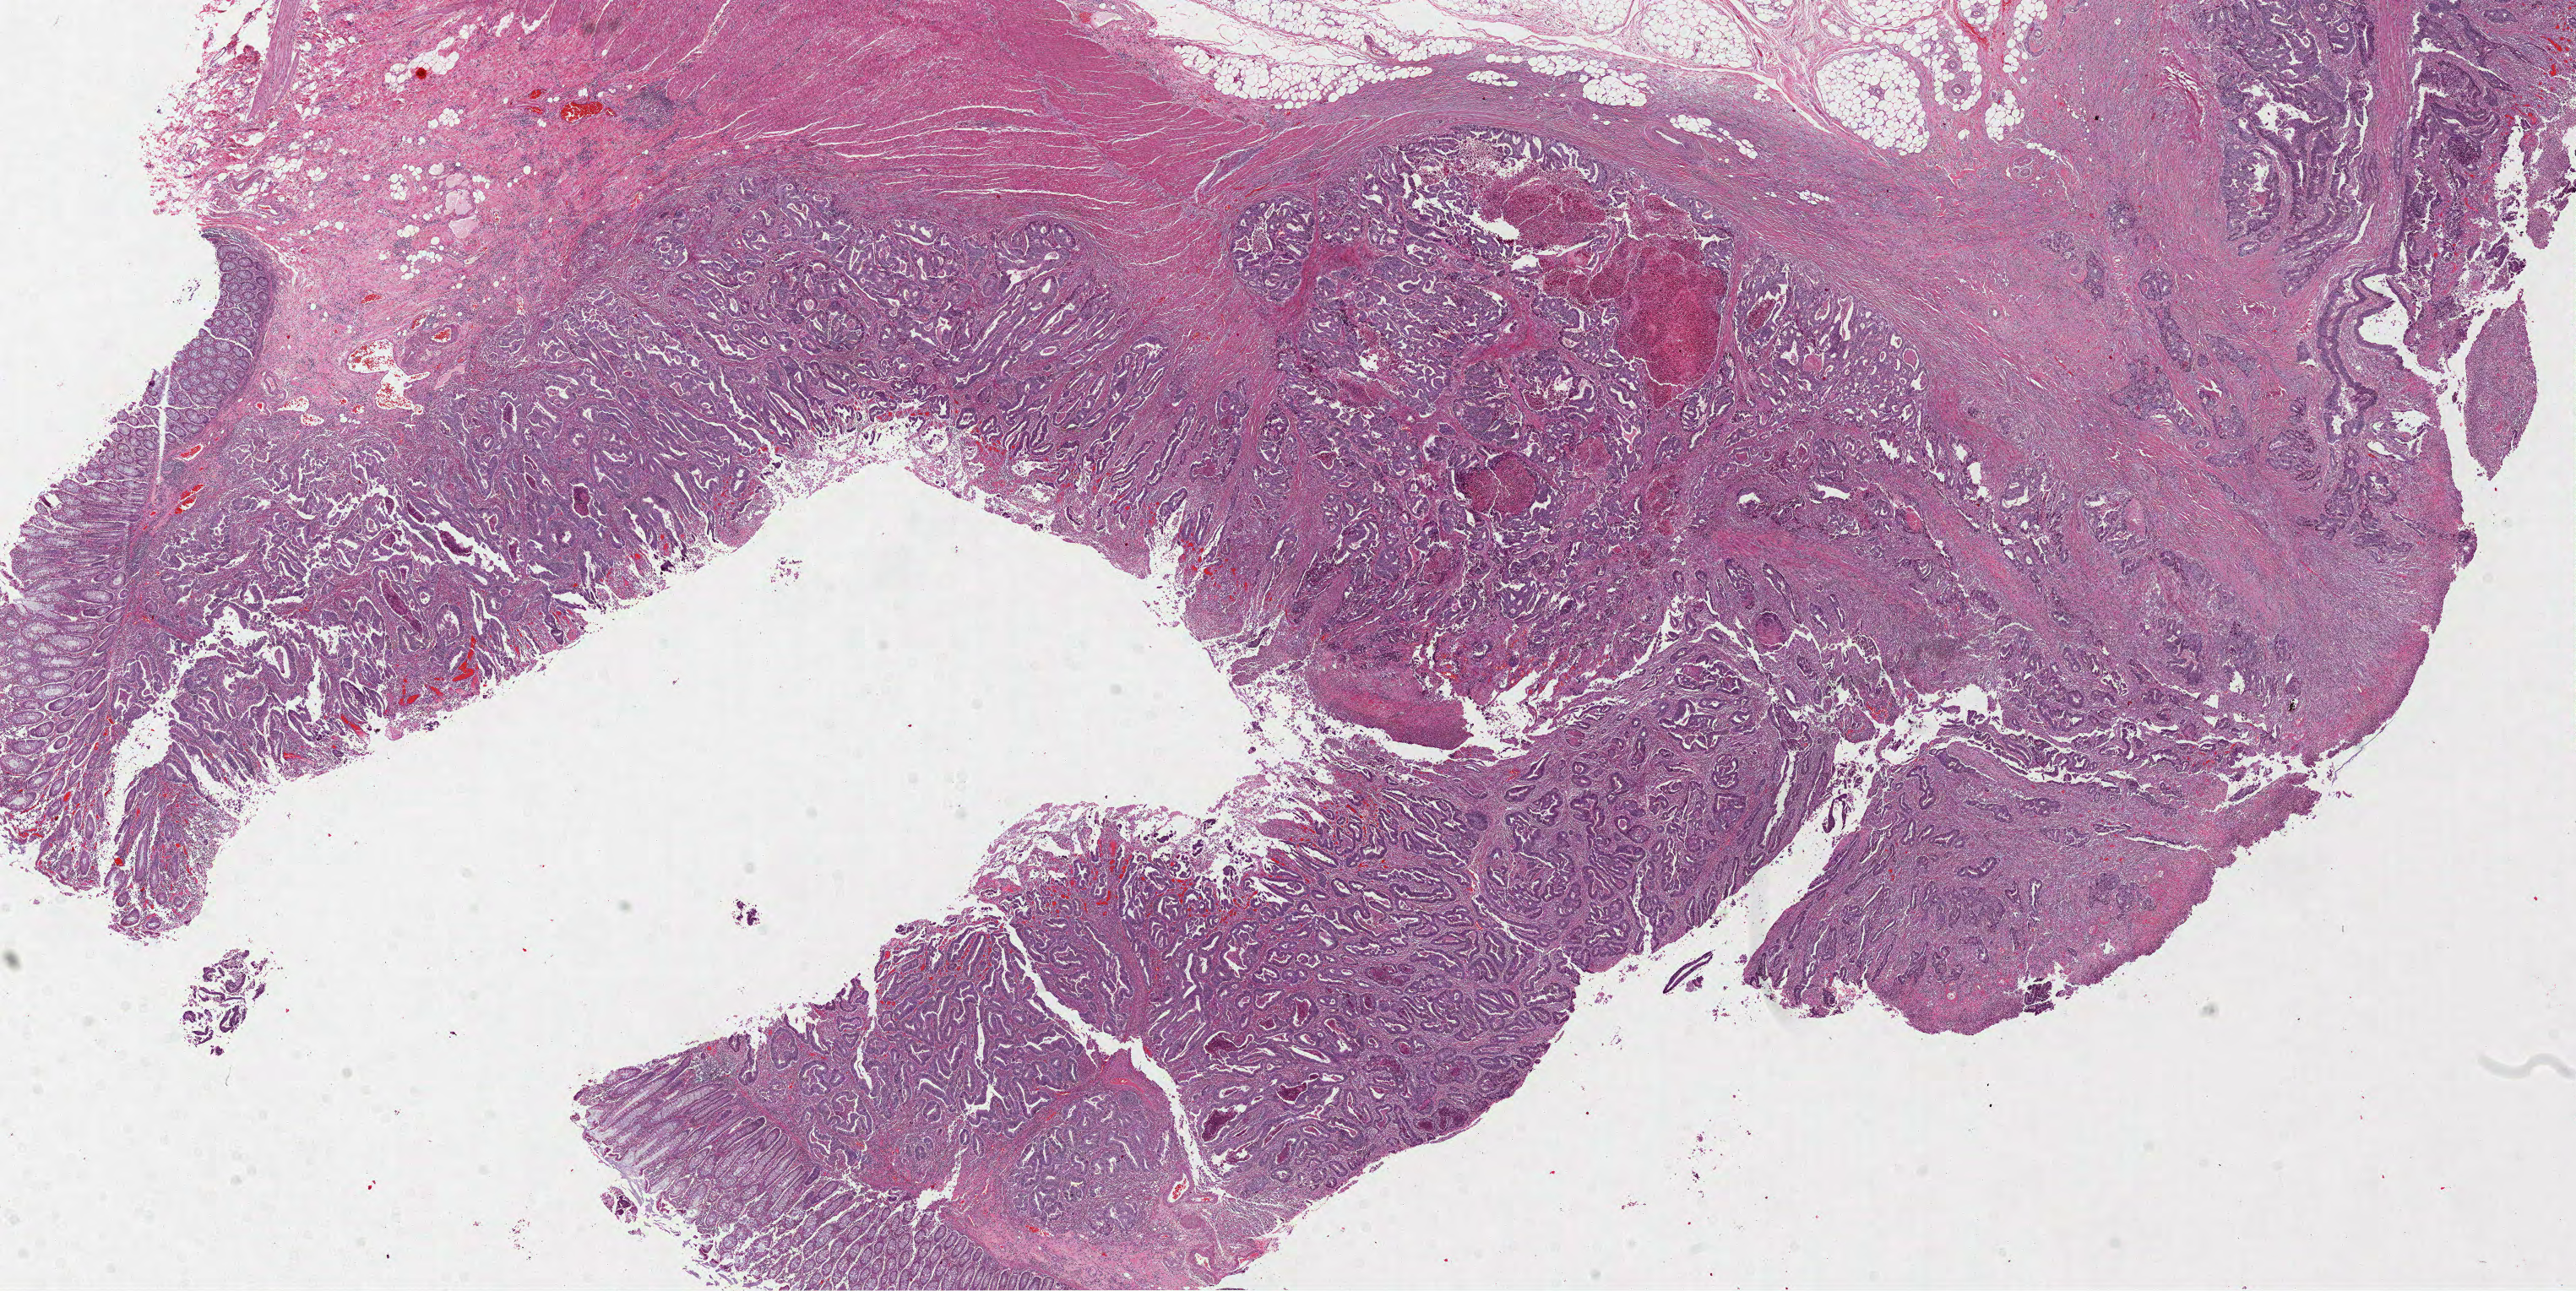
Digitized Hematoxylin and eosin (H&E) stained tissue section (whole slide), whole scanned area (about 24.6 x 12.3 mm) shown as a low-resolution overview, FFPE section, colon, primary tumour sample. Male, age 58 years at initial diagnosis.
Diagnosis: Adenocarcinoma, NOS (ascending colon). TNM: T3 N0 M0. Lymph nodes positive (case pathology): 0 of 23 examined. AJCC pathologic stage: IIA.